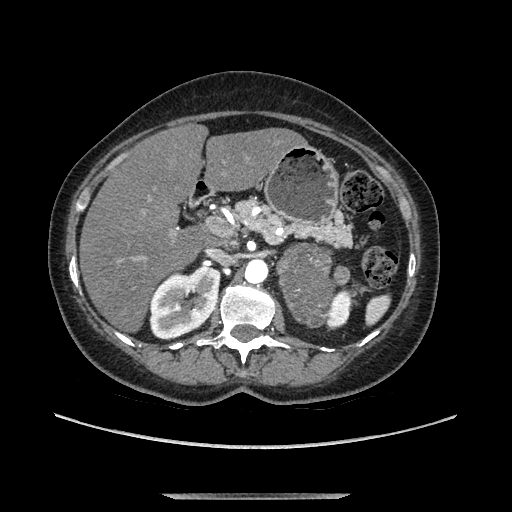
Contrast-enhanced abdominal CT, one axial slice; position 69 of 169 along the scan axis; soft-tissue window (W 400 / L 40 HU); 1.25 mm slice thickness; 512 × 512 image matrix, field of view 400 × 400 mm. Female patient. From the clinical record (not read from this slice): diagnosis: adrenocortical carcinoma; tumour side: left adrenal; tumour size at pathology: 9 cm; Ki-67 index: 2 %; stage (as recorded): 3.
Annotated regions visible in this slice (semi-automatically segmented with operator editing):
- mass: bounding box <279,246,333,326> (left, top, right, bottom; pixels)